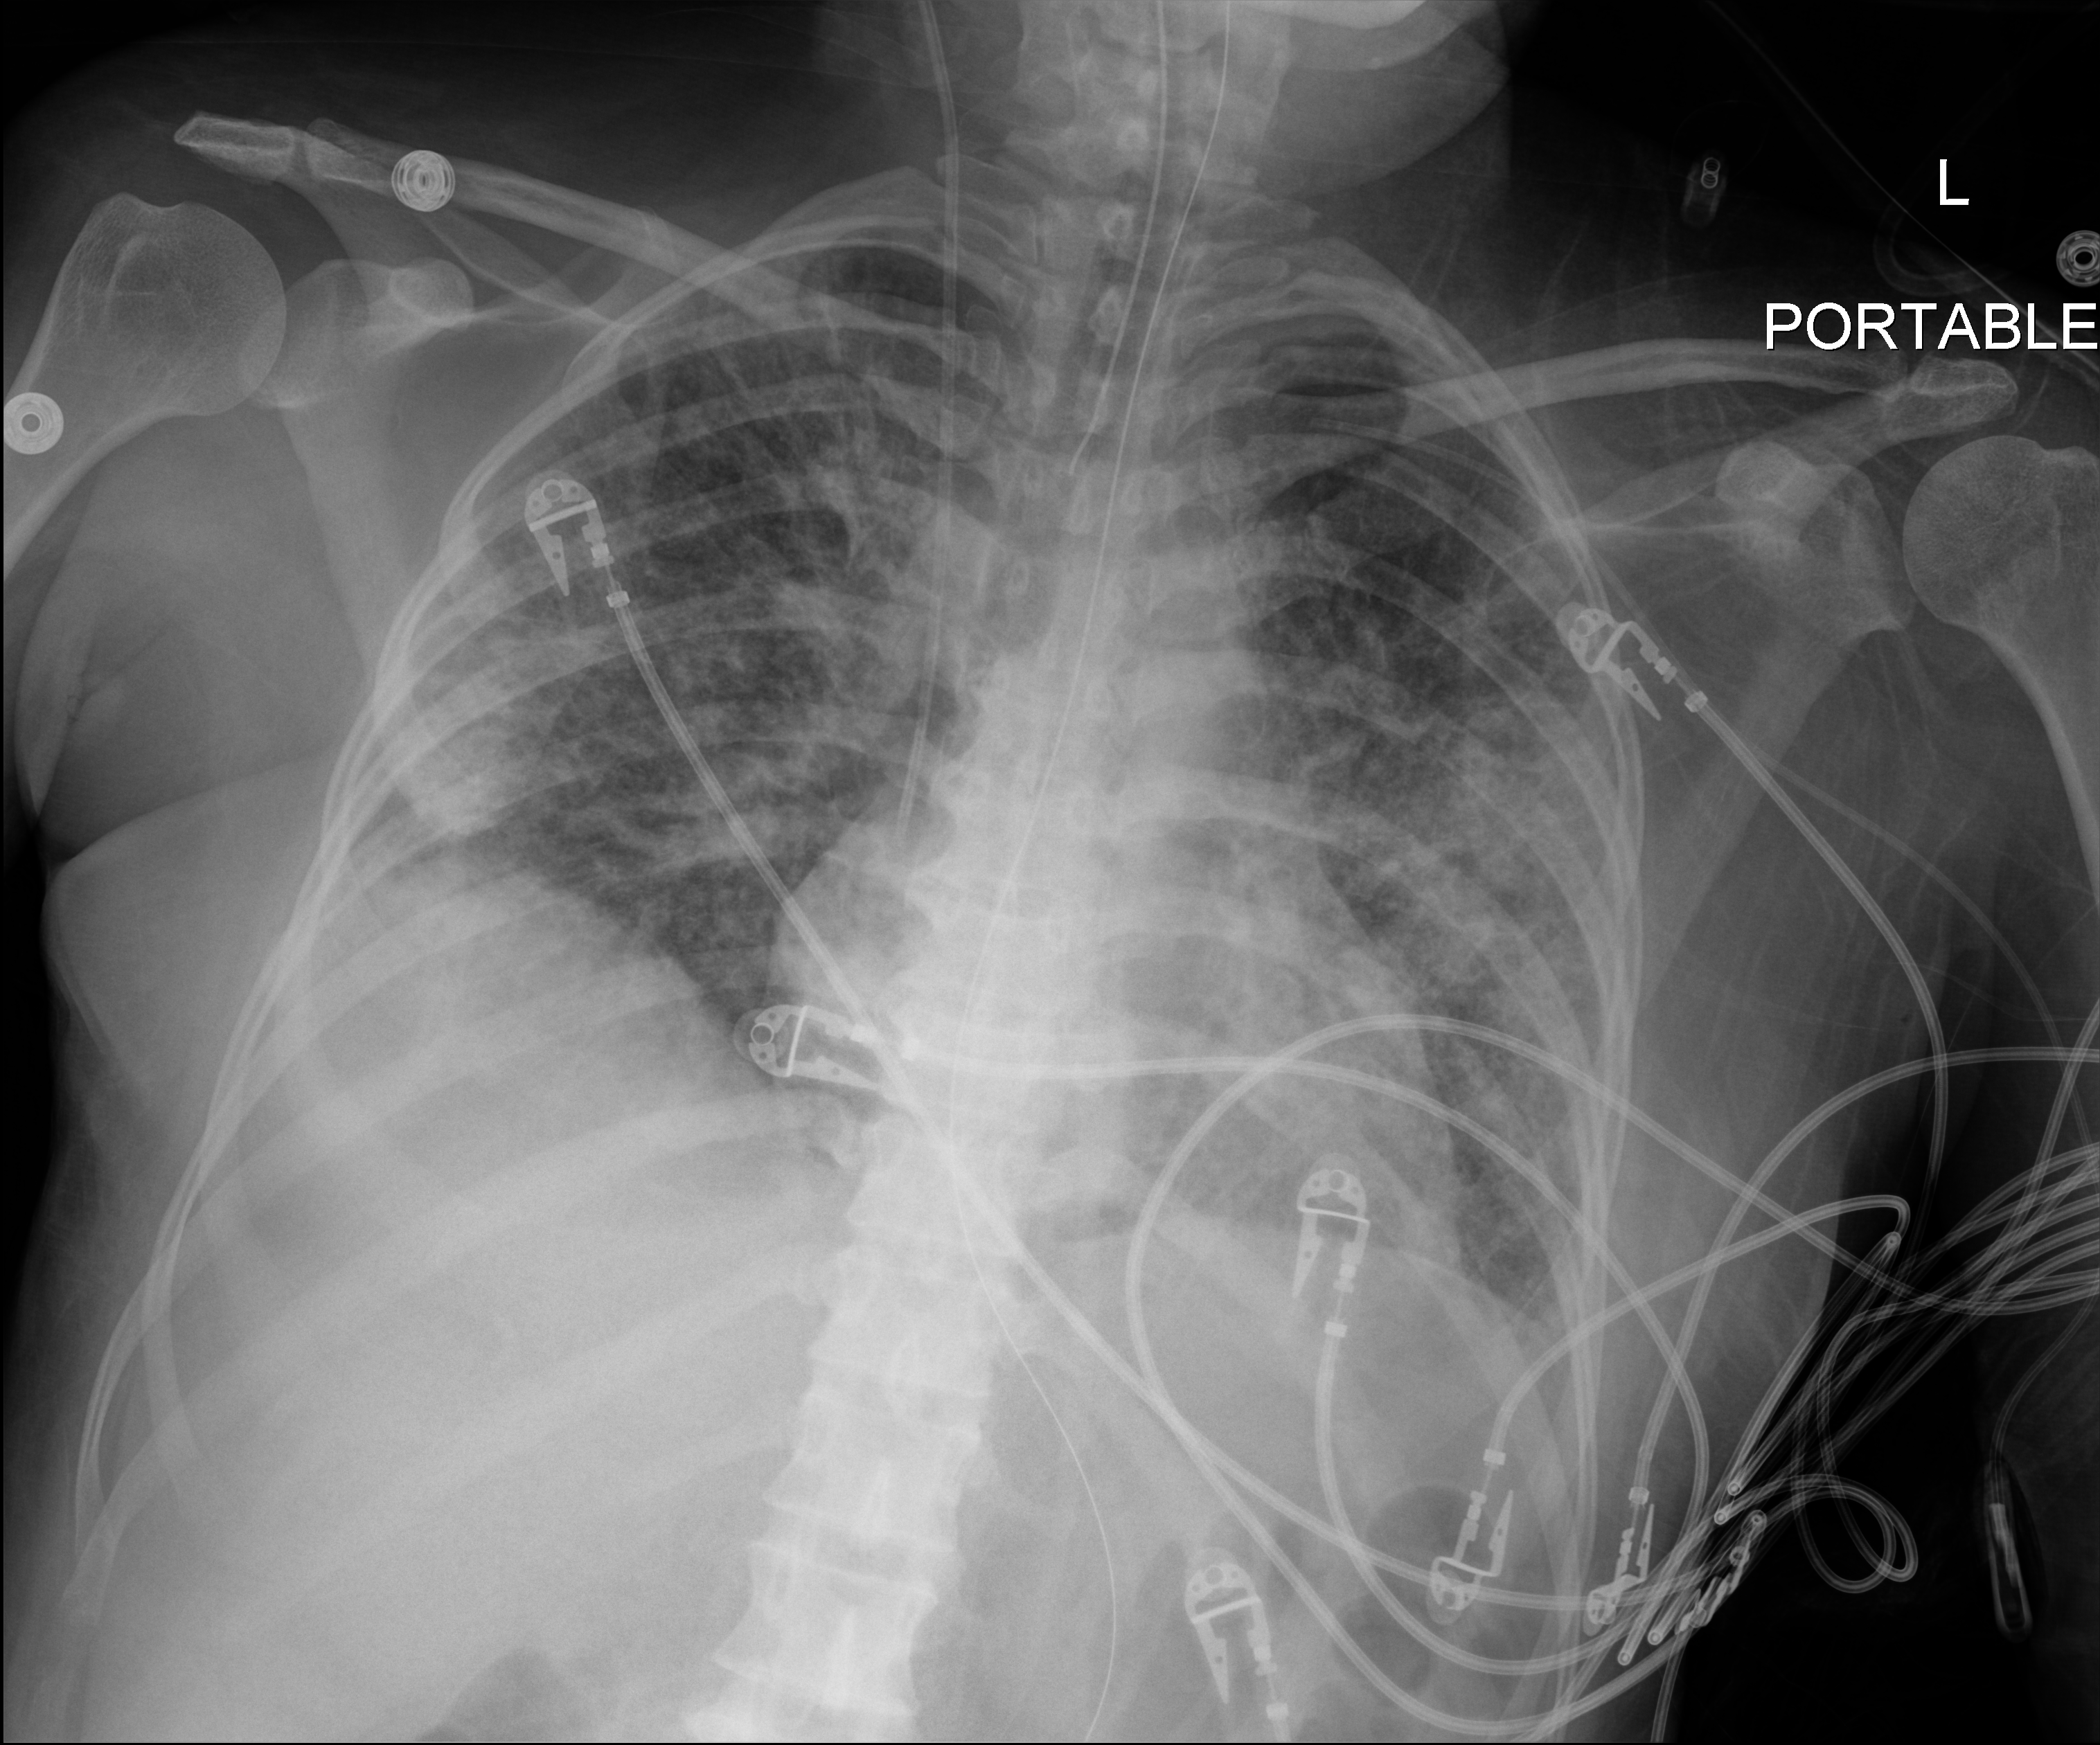
Chest X-ray (portable); anteroposterior (AP) projection. Patient hospitalised with COVID-19; female, aged 18–59 years.
From the hospital-stay record, not from the radiograph (when in the stay this image was taken is not recorded): admitted to intensive care during this hospital stay: yes; mechanically ventilated during this hospital stay: yes; hypertension (admission record): no.